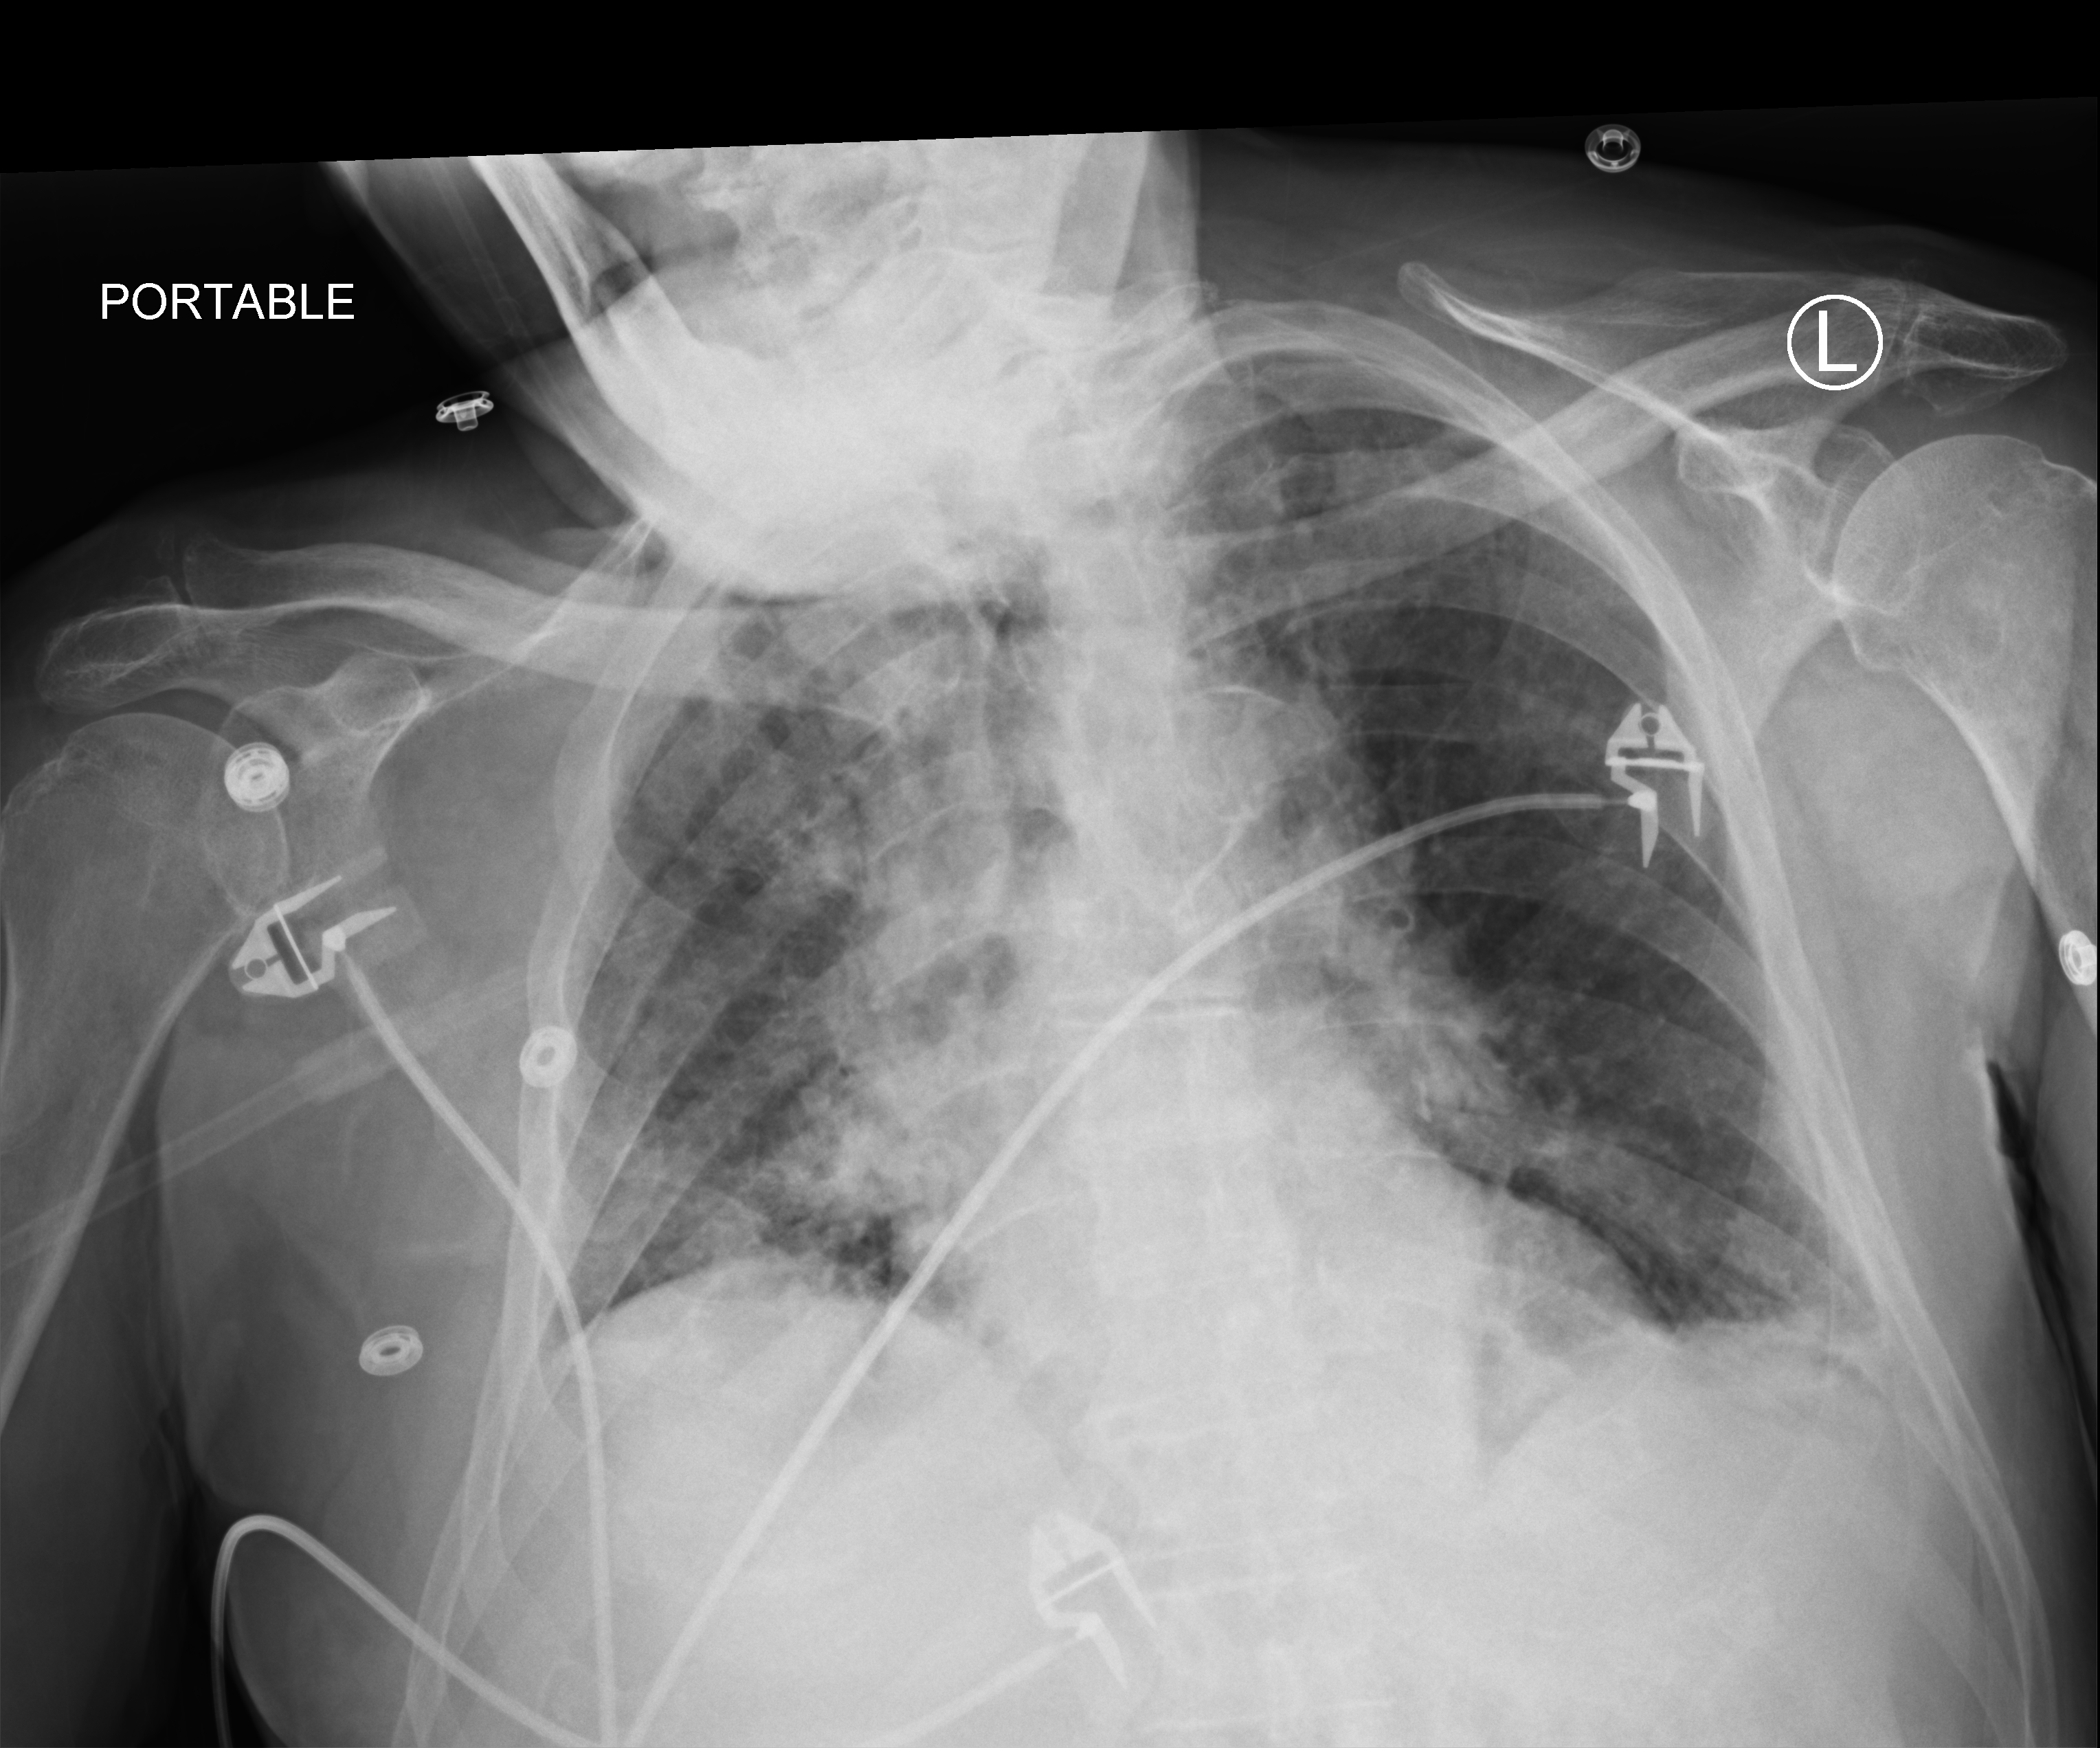
Chest X-ray (portable); anteroposterior (AP) projection. Patient hospitalised with COVID-19; male, aged 75–90 years.
From the hospital-stay record, not from the radiograph (when in the stay this image was taken is not recorded): length of hospital stay: 28 days.